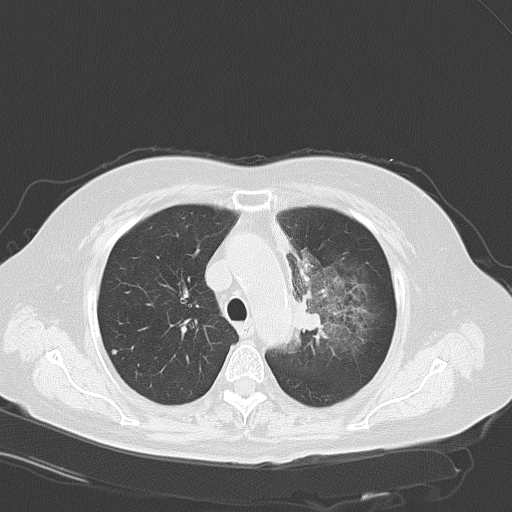
Chest CT, one axial slice. Reconstruction kernel B70f. 120 kVp. Lung window (W 1500 / L -600 HU). 5 mm slice thickness. 512 × 512 image matrix, field of view 353 × 353 mm. Patient: female, 65 years. Case-level facts recorded for this patient, not image findings: clinical TNM (as recorded): T2b N1 M0.
Outlined on this slice (bounding box drawn by a radiologist):
- lung tumour (recorded histology: adenocarcinoma): bounding box (x1, y1, x2, y2) in pixels: (295, 294, 329, 342)